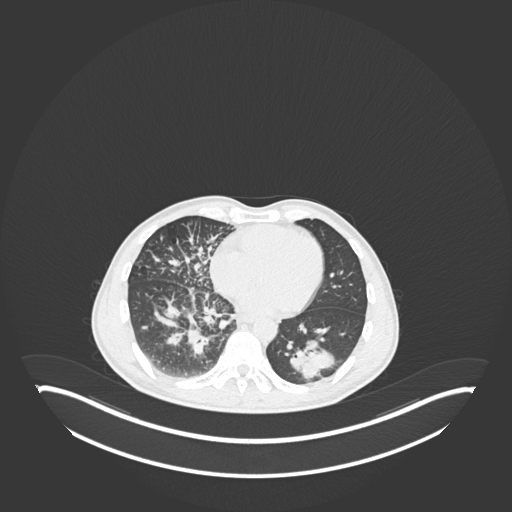
Chest CT, one axial slice; slice 85 of 237 in the series (ordered by position); reconstruction kernel B30f; 120 kVp; lung window (W 1500 / L -600 HU); 512 × 512 image matrix, field of view 500 × 500 mm. Patient: male, 49 years. Case-level facts recorded for this patient, not image findings: clinical TNM (as recorded): T2b N1 M0.
Annotated regions visible in this slice (bounding box drawn by a radiologist):
- lung tumour (recorded histology: adenocarcinoma): bounding box (x1, y1, x2, y2) in pixels: (286, 335, 336, 384)